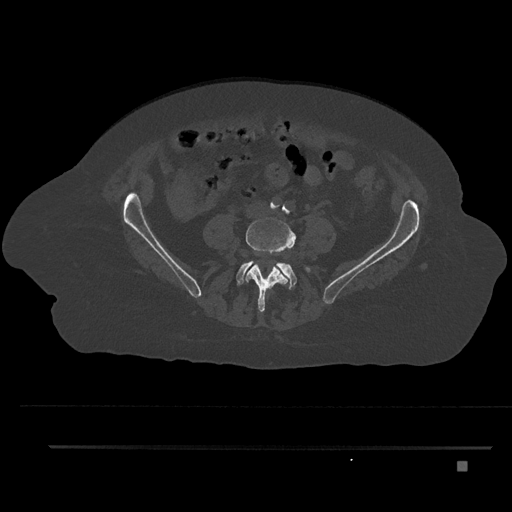
CT including the spine, one axial slice. Slice 65 of 797 in the series (ordered by position). Bone window (W 1800 / L 400 HU). 0.5 mm slice thickness. 512 × 512 image matrix. Female patient, age 76 years. From the clinical record (not read from this slice): primary cancer: lung; vertebrae with lytic lesions (as recorded): T11, L3.
Outlined on this slice (semi-automatically segmented with operator editing):
- L4 vertebra: bounding box <246,217,295,312> (left, top, right, bottom; pixels)
- L5 vertebra: <237,261,310,289>